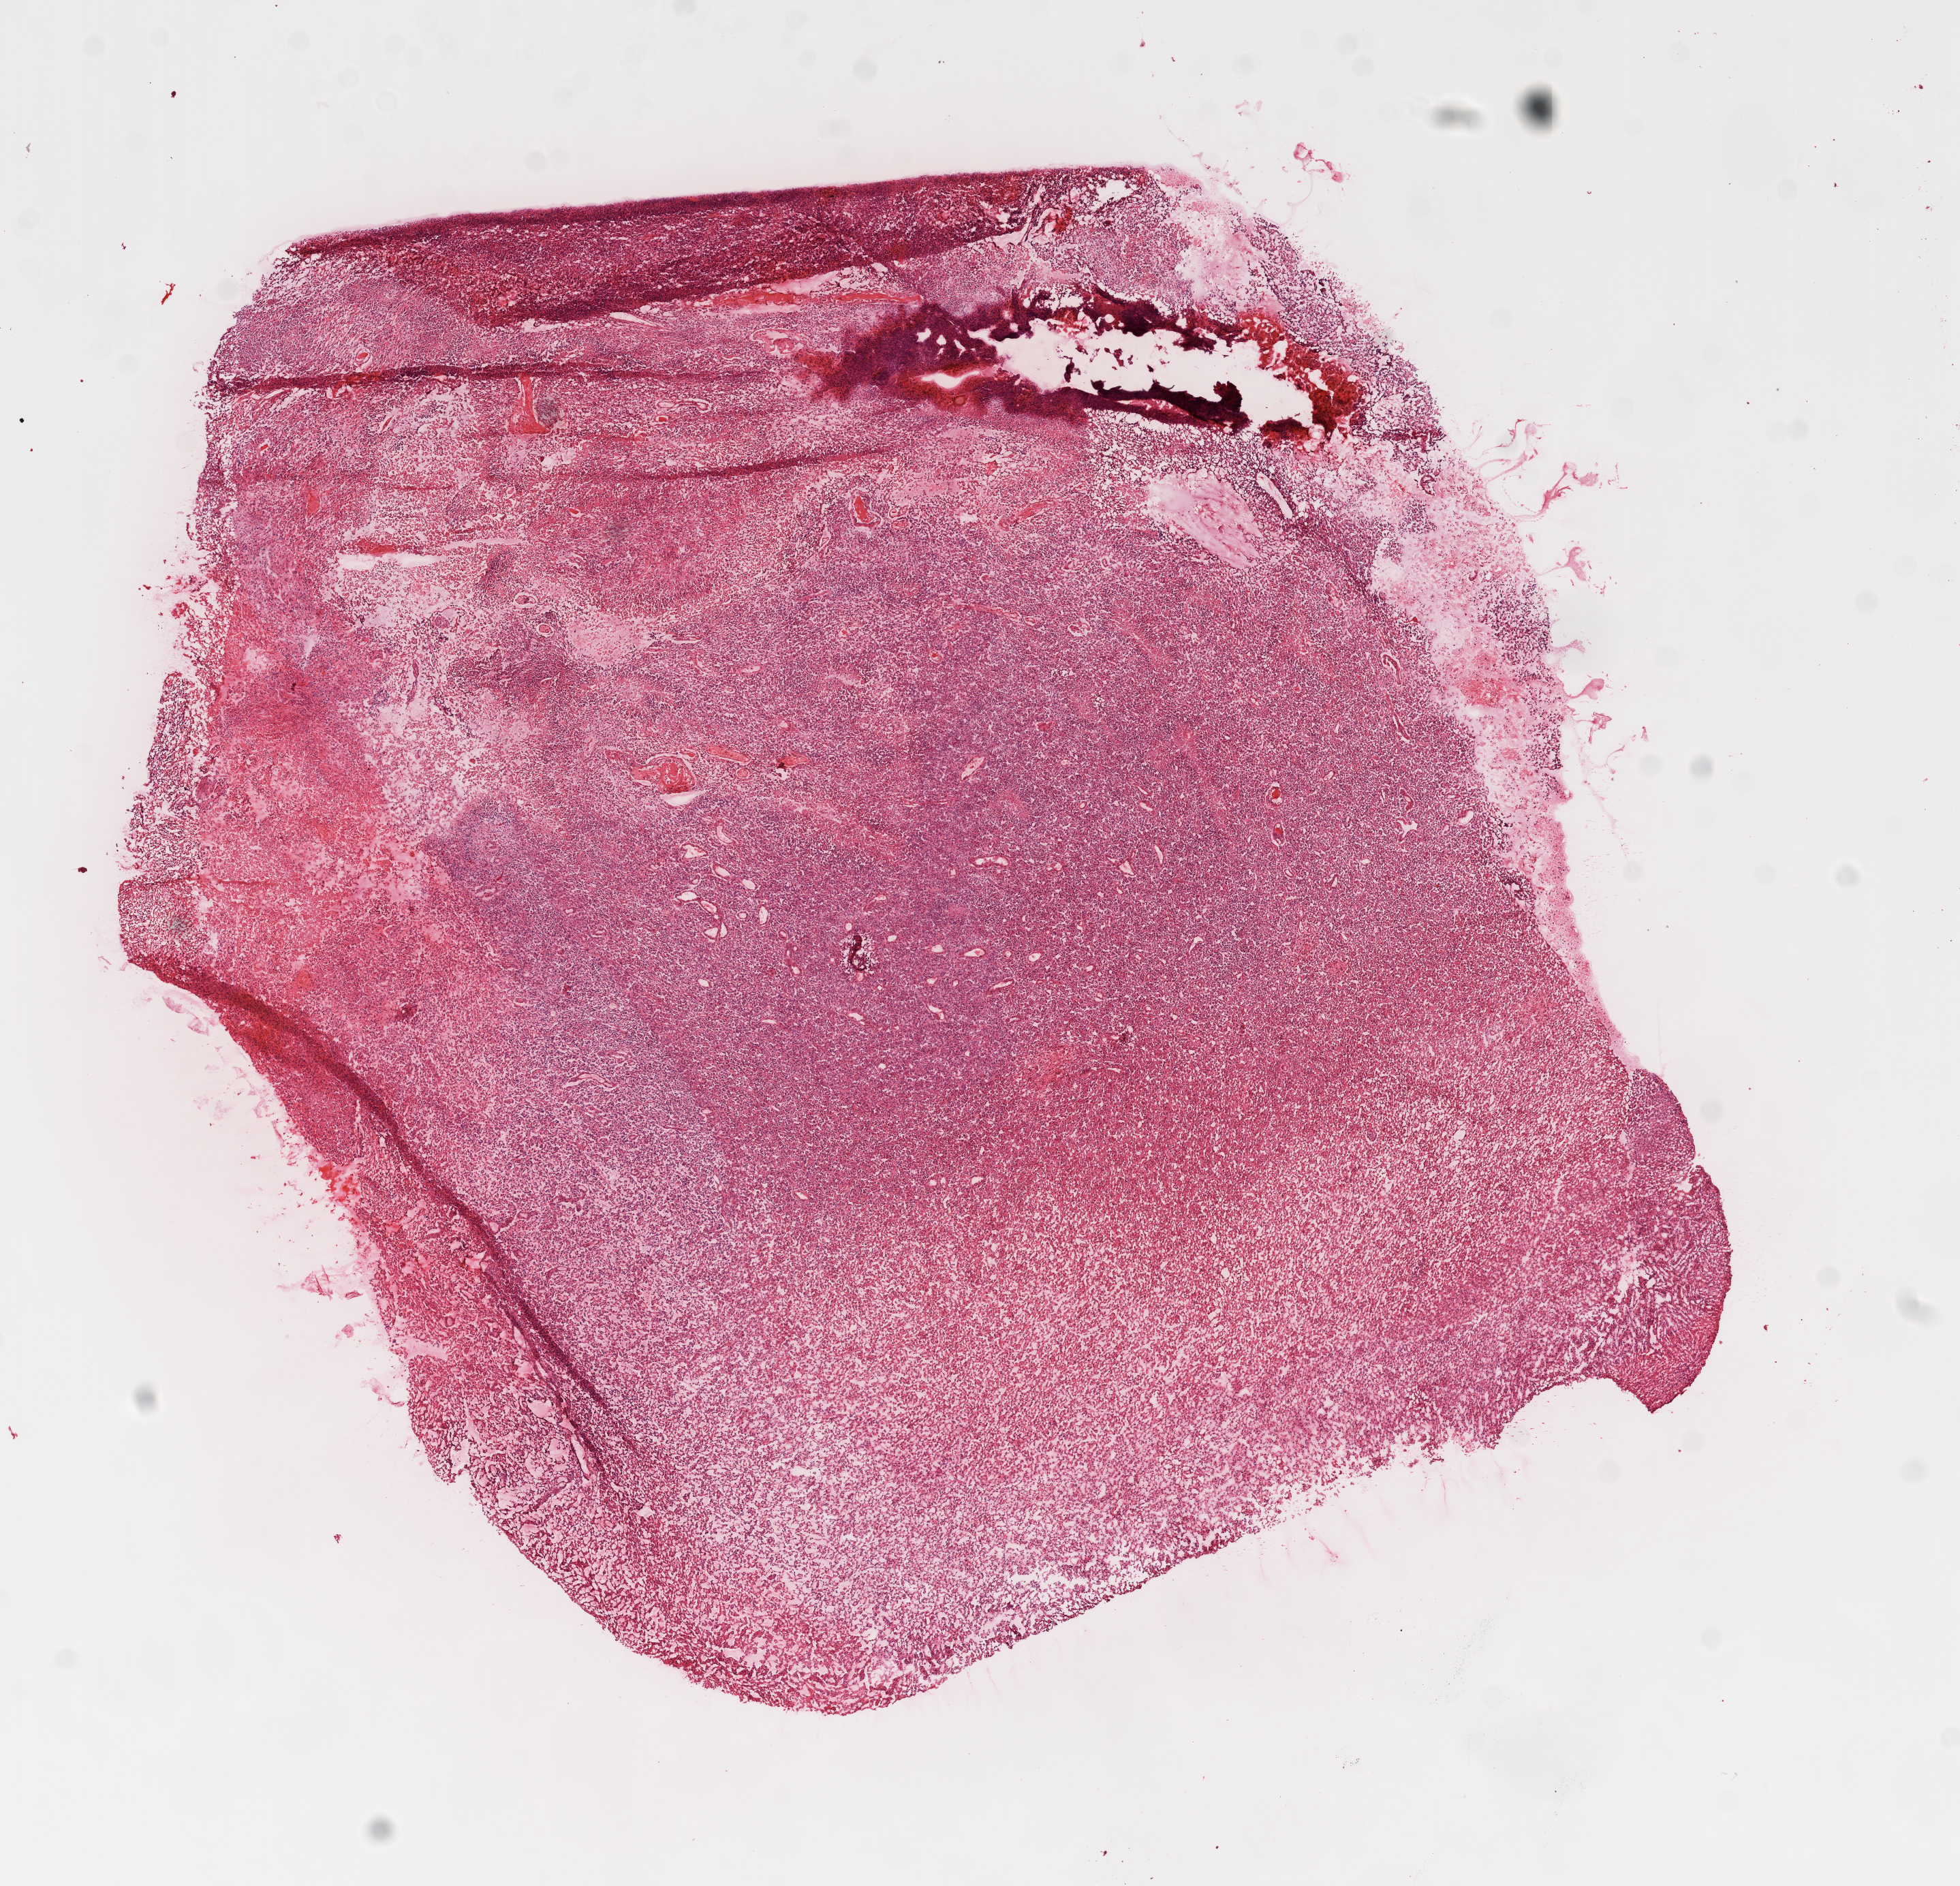
H&E-stained whole-slide image — shown as a low-resolution overview of the whole scanned area (about 11.6 x 11.2 mm), frozen section from the top of the tissue portion, primary tumour sample from the brain. Patient: female, age at initial diagnosis 10 years. Slide review estimates, as recorded: tumour cells 90%, tumour nuclei 95%, stromal cells 5%, necrosis 5%.
Pathologic diagnosis: Glioblastoma.